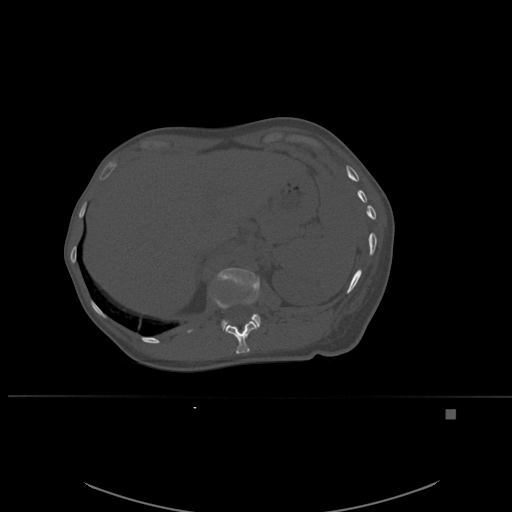
CT including the spine, one axial slice. Position 271 of 537 along the scan axis. Bone window (W 1800 / L 400 HU). 1.5 mm slice thickness. 512 × 512 image matrix. Patient: female, 45 years. From the clinical record (not read from this slice): primary cancer: lung.
Annotated regions visible in this slice (semi-automatically segmented with operator editing):
- L1 vertebra: bounding box [x1, y1, x2, y2] px = [216, 268, 261, 331]
- T12 vertebra: [213, 278, 257, 354]